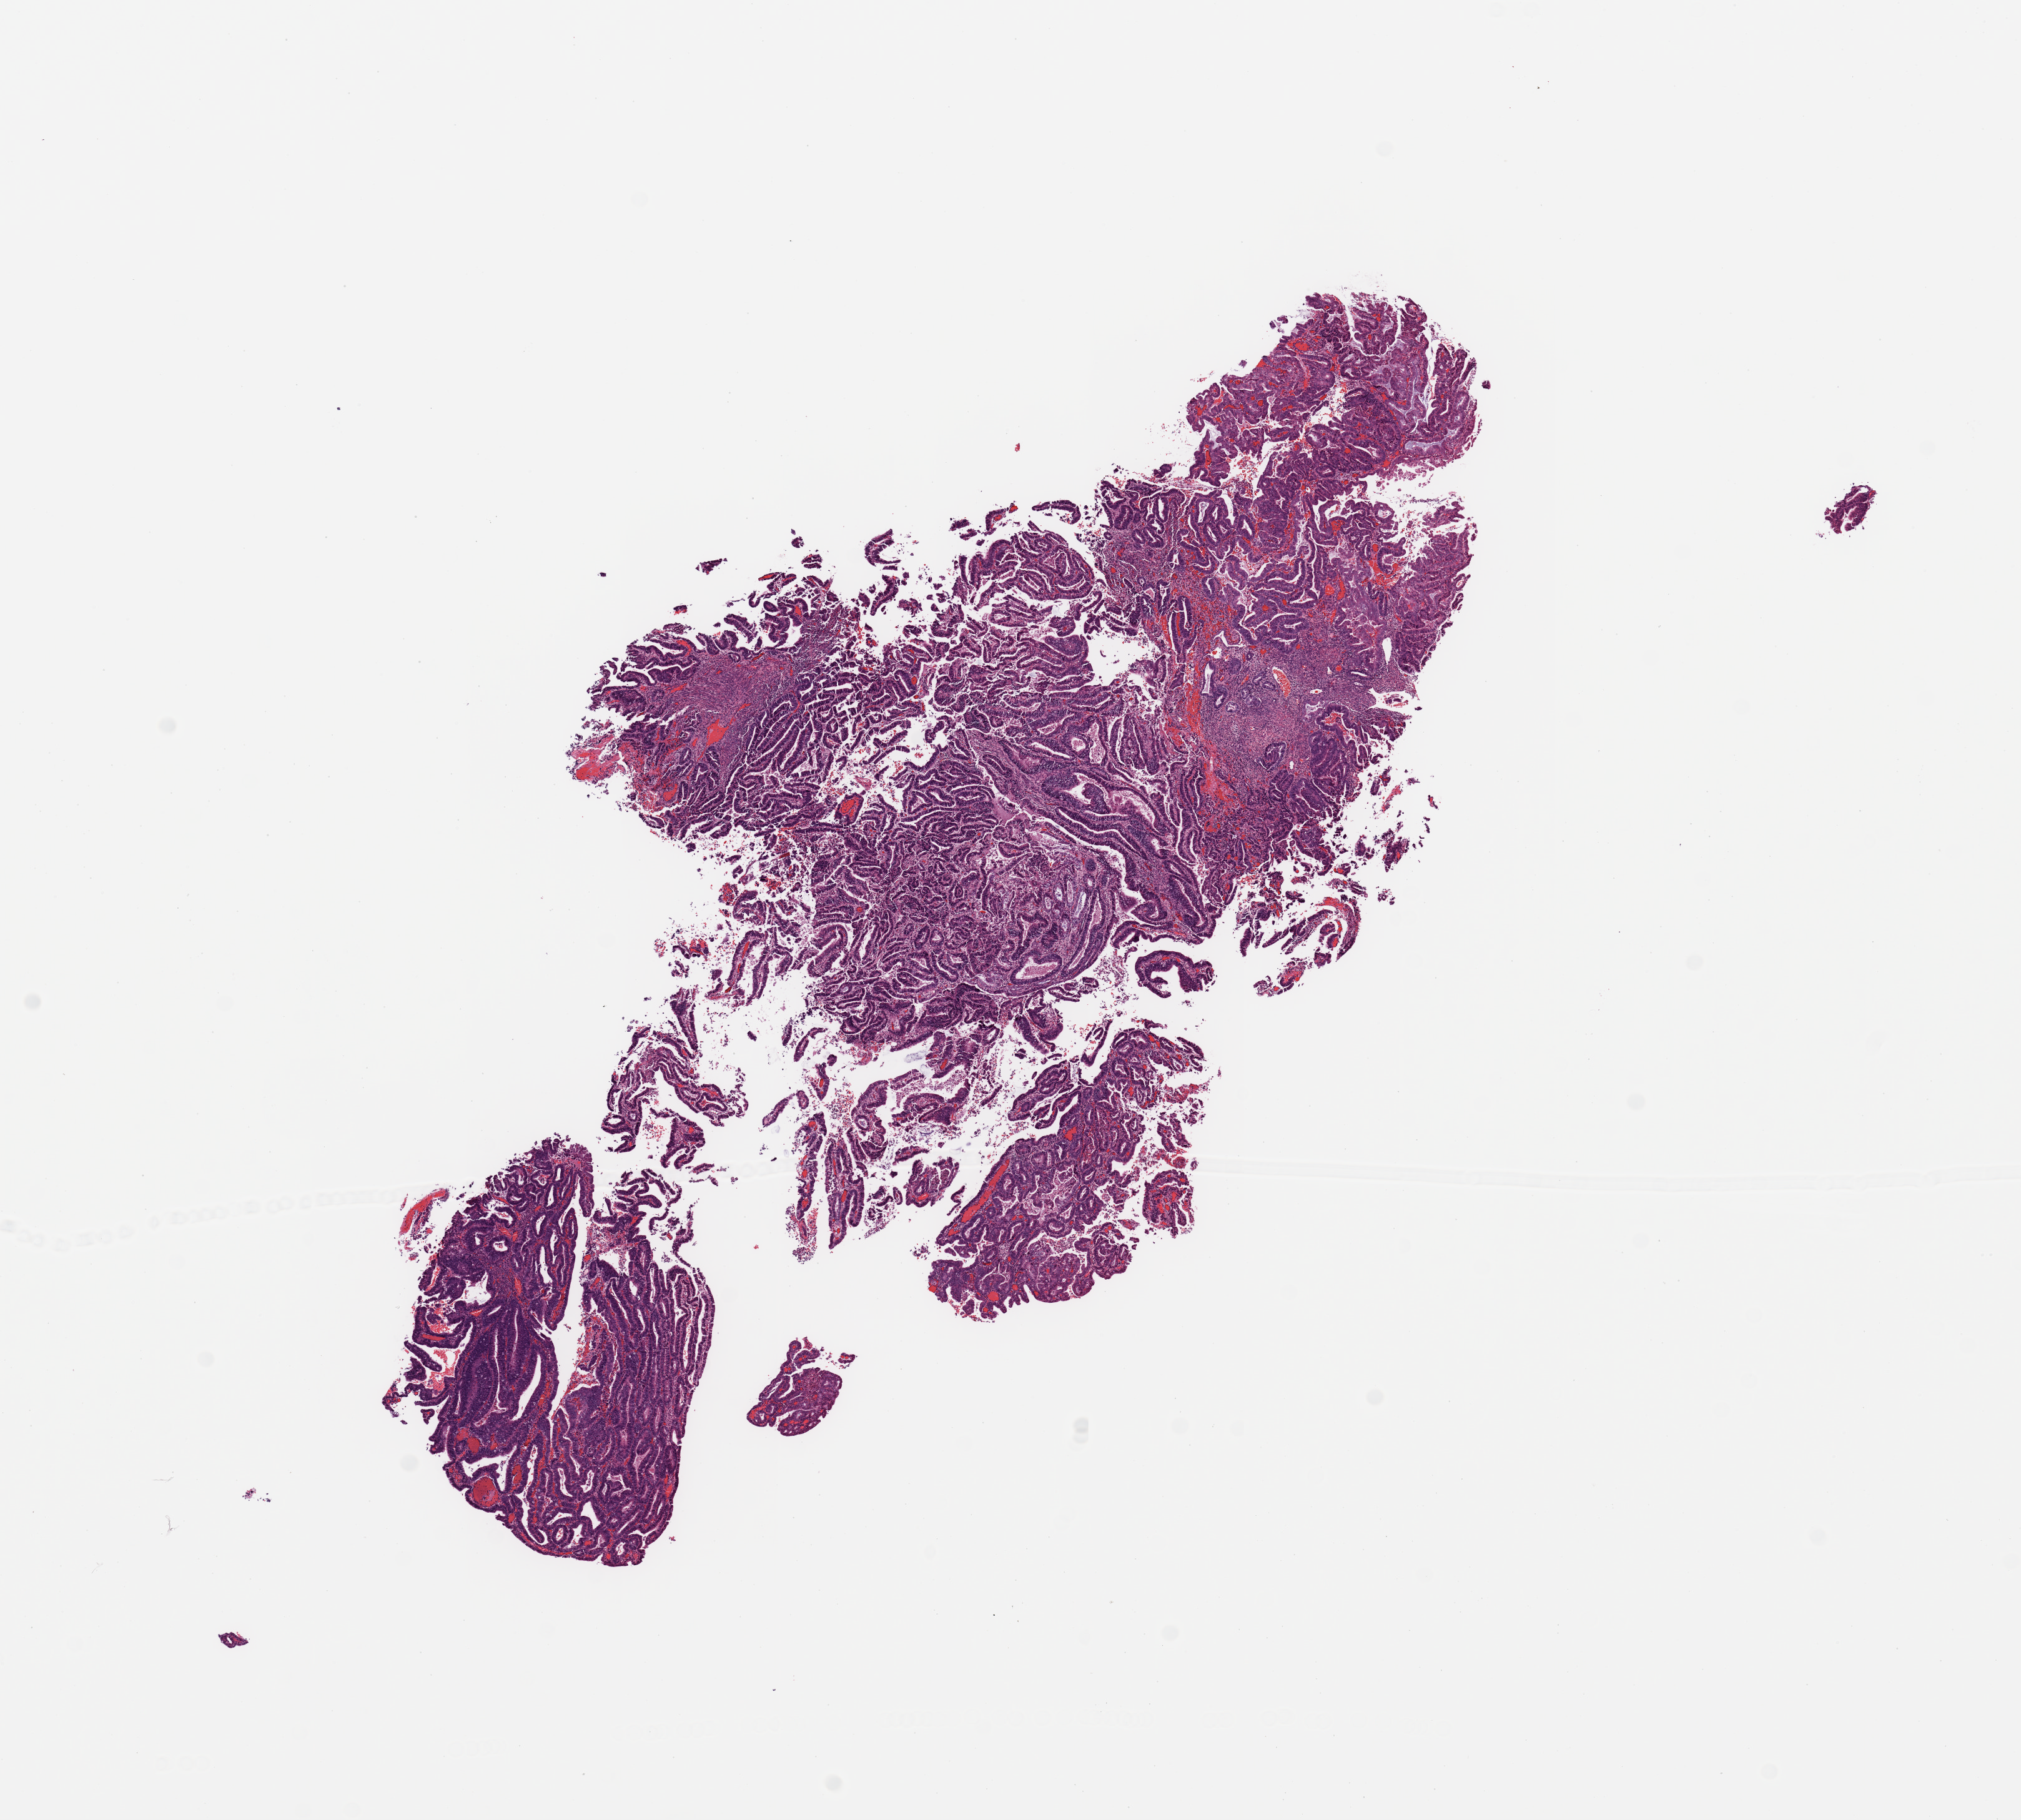
Digitized Hematoxylin and eosin (H&E) stained tissue section (whole slide), low-resolution overview of the scanned area, about 12.8 x 11.5 mm; tumour tissue sample, sampled site: uterus. 71-year-old female patient. Histologic grade: G1 (well differentiated). Composition of this section per pathologist review: tumour nuclei 90%, necrosis 2%.
AJCC pathologic stage: III. Primary tumour site (as recorded): anterior endometrium. Histologic diagnosis: Endometrioid adenocarcinoma, NOS.